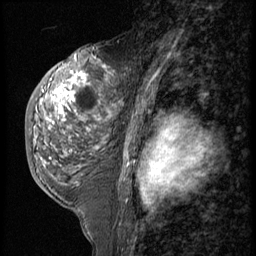
Breast MRI (dynamic contrast-enhanced), one sagittal slice; slice 33 of 56 in the series (ordered by position); 3 images stored at this slice position (order not interpretable as contrast timing); 1.5 T; TE 4.2 ms, TR 9 ms; 256 × 256 image matrix, field of view 180 × 180 mm. Patient: female, 50 years. Case-level facts recorded for this patient, not image findings: setting: breast cancer imaged before/during neoadjuvant chemotherapy; receptor status: triple-negative.
Outlined on this slice (semi-automatic segmentation, software-assisted and operator-edited):
- analysis volume of interest (the breast-tissue region the enhancement analysis was run in; not a lesion): box from (x=25, y=50) to (x=120, y=191) px
- tumour enhancement mask (voxels above the 140 % enhancement threshold inside the analysis volume of interest): (x=43, y=67)–(x=110, y=150)